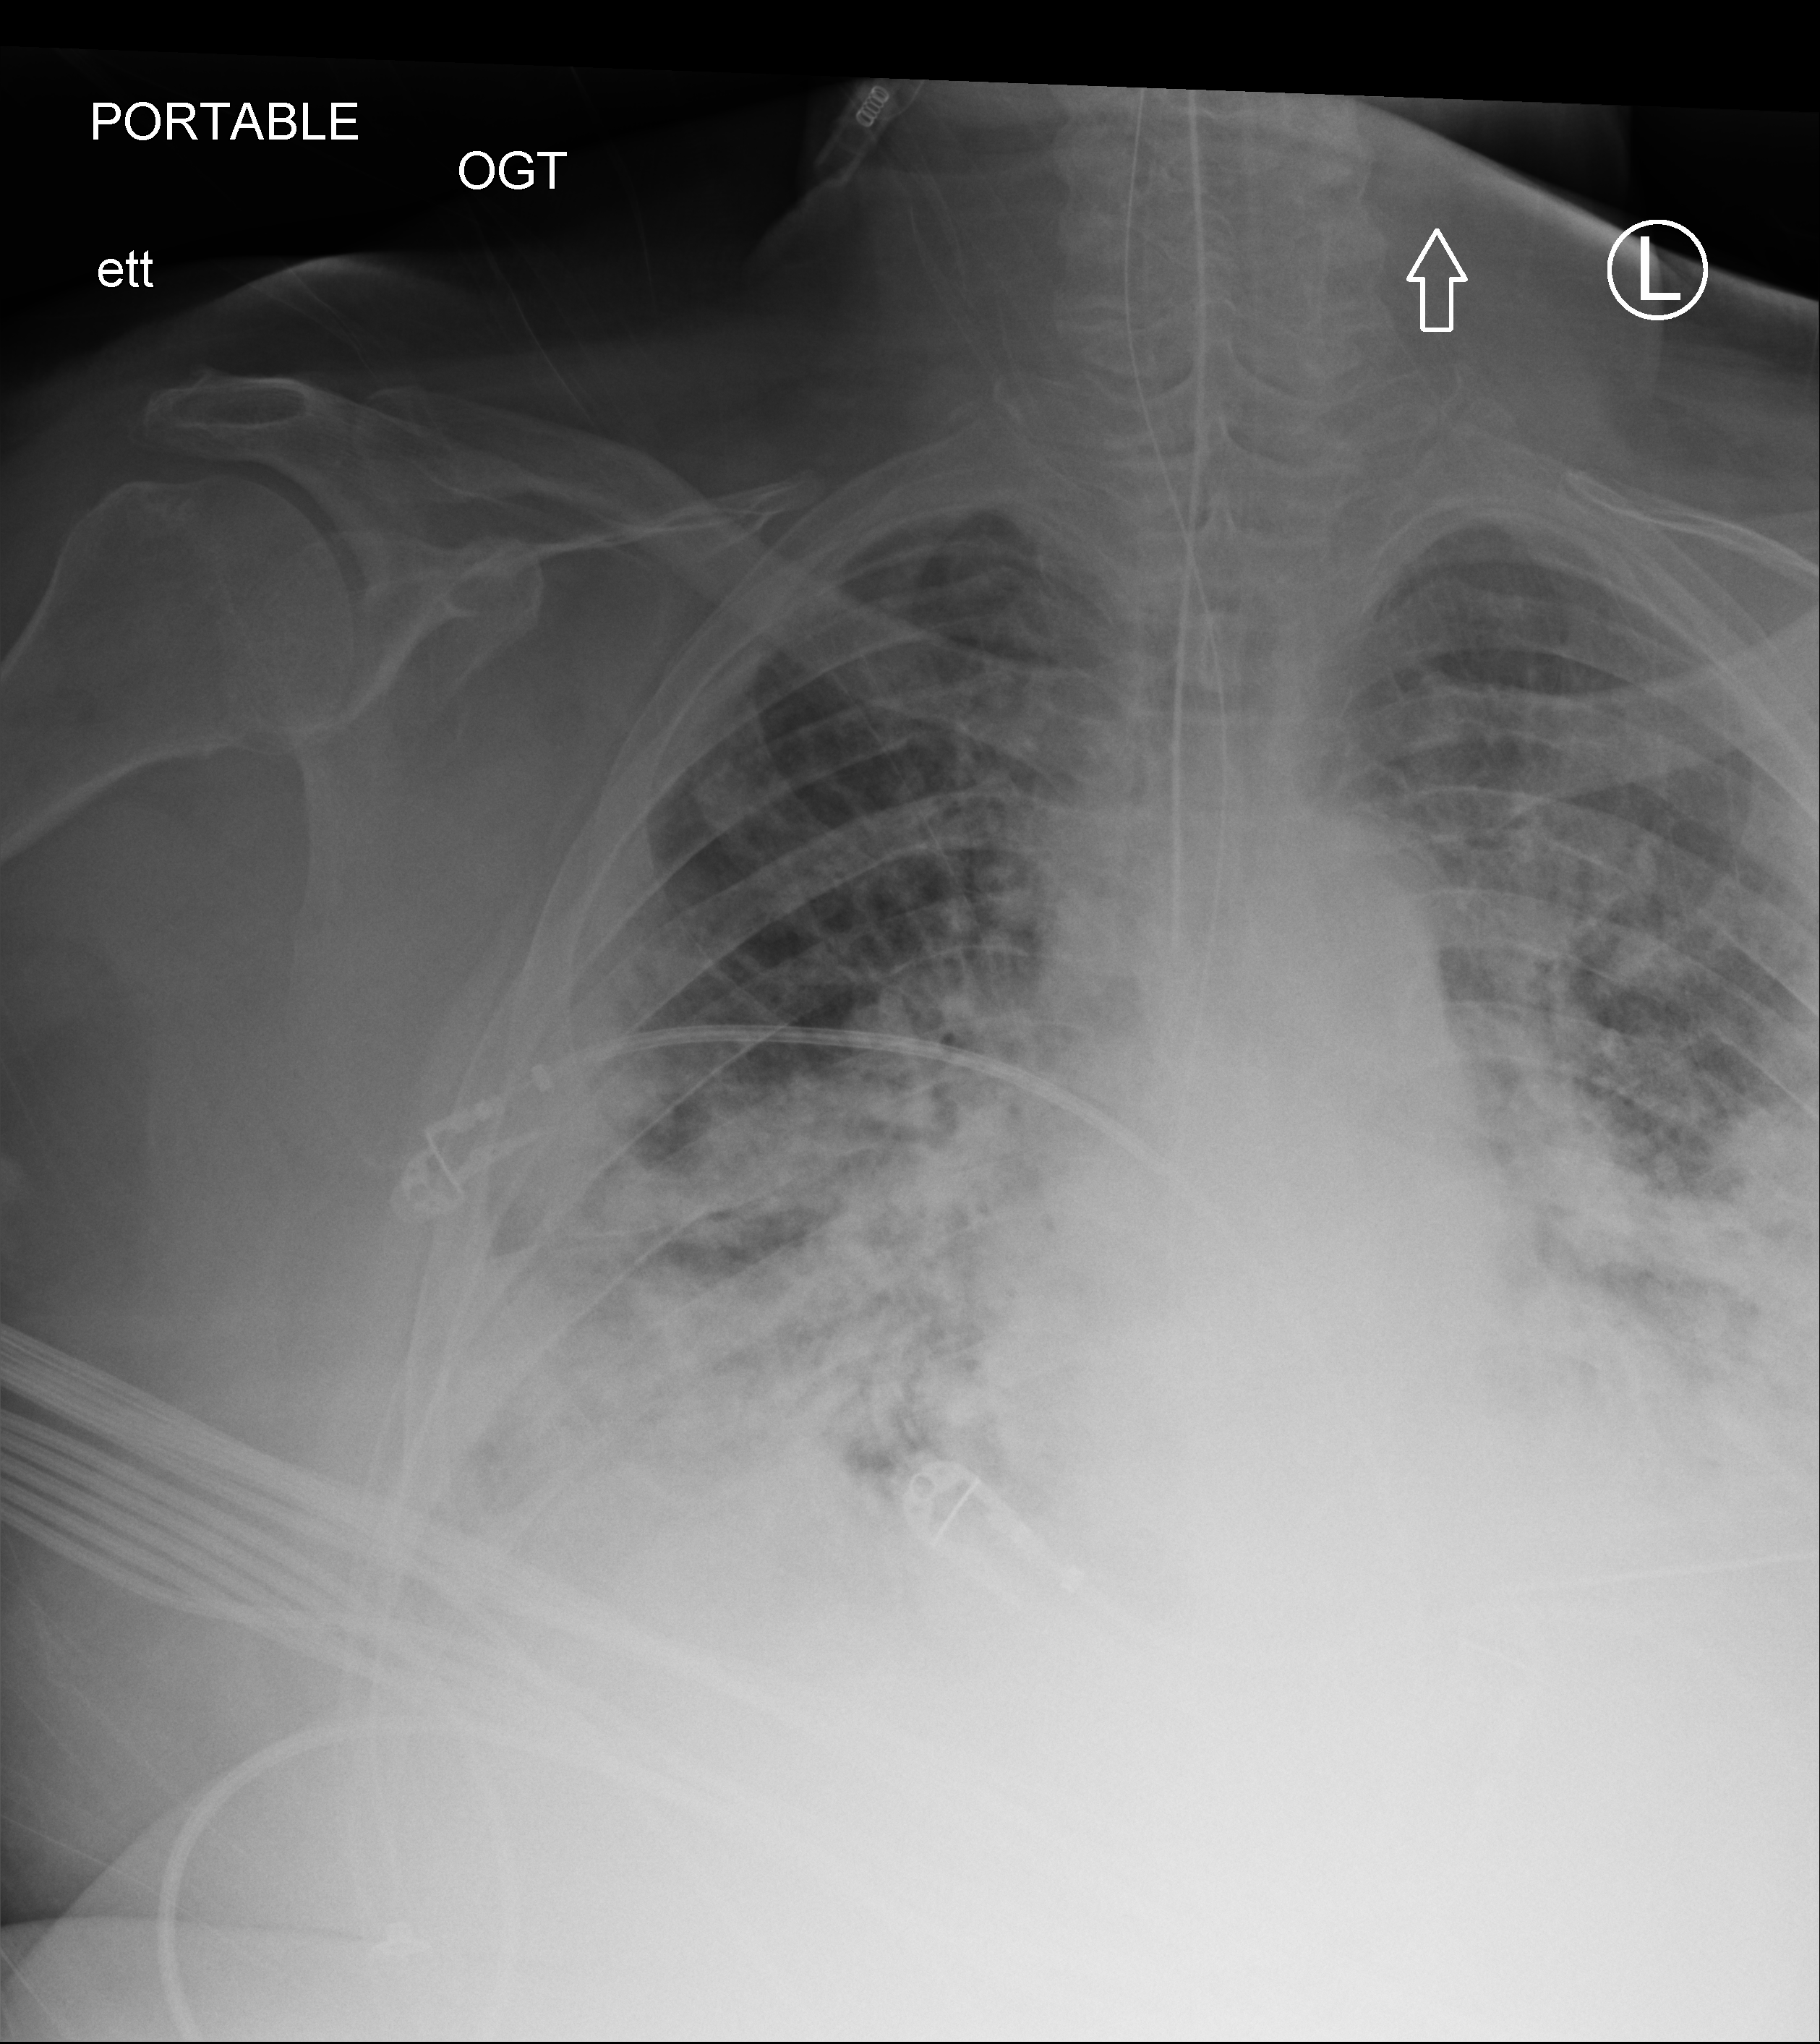
Bedside chest radiograph (computed radiography), anteroposterior (AP) projection. Patient hospitalised with COVID-19; male, aged 60–74 years.
Hospital-stay facts (about this admission, not read from this image; timing relative to this image not recorded): COPD (admission record): no; hypertension (admission record): yes; mechanically ventilated during this hospital stay: yes.